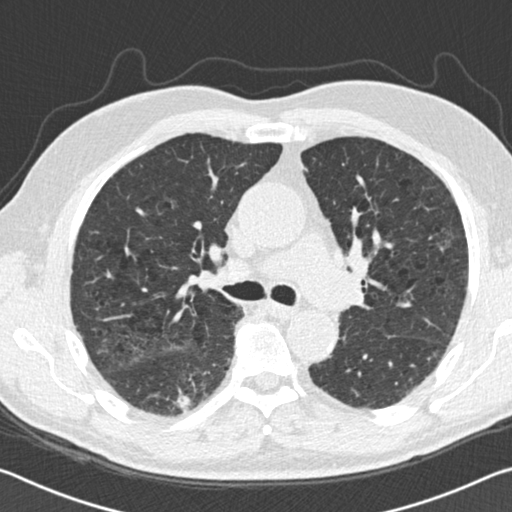
Axial slice from a low-dose chest CT screening exam, second annual screen, lung window (W 1500 / L -600 HU), 2 mm slice thickness, standard (soft-tissue) reconstruction kernel (B30f), slice 57 of 142 in the series, 512 × 512 image matrix. Male participant, aged 69 years at enrolment. Current smoker at enrolment.
• Lesion marked by an expert reader, box from (x=160, y=377) to (x=208, y=424) px.
• The exam's reader record, not a measurement of the box and not confirmed to be the same lesion: non-calcified nodule or mass ≥4 mm, right lower lobe, 10 × 10 mm, spiculated (stellate) margins, soft tissue attenuation, pre-existing on the prior screen: yes; interval growth: yes.
• Official screen result: positive, other.
• Later outcome: lung cancer diagnosed 290 days after this screen — squamous cell carcinoma, NOS, right lower lobe, moderately differentiated (G2), stage IA (AJCC 6th edition), 25 mm at pathology.